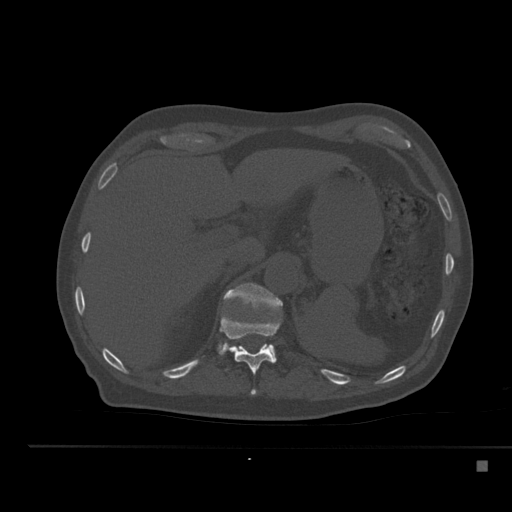
CT including the spine, one axial slice. Slice 245 of 517 in the series (ordered by position). Reconstruction kernel Br40s. 120 kVp. Bone window (W 1800 / L 400 HU). 1.5 mm slice thickness. 512 × 512 image matrix, field of view 408 × 408 mm. Patient: male, 70 years. Case-level facts recorded for this patient, not image findings: primary cancer: renal; vertebrae with lytic lesions (as recorded): T4, T6, T10, T12, L3, L4, L5.
Annotated regions visible in this slice (semi-automatic segmentation, software-assisted and operator-edited):
- T11 vertebra: box from (x=219, y=314) to (x=281, y=396) px
- T12 vertebra: (x=224, y=283)–(x=283, y=360)